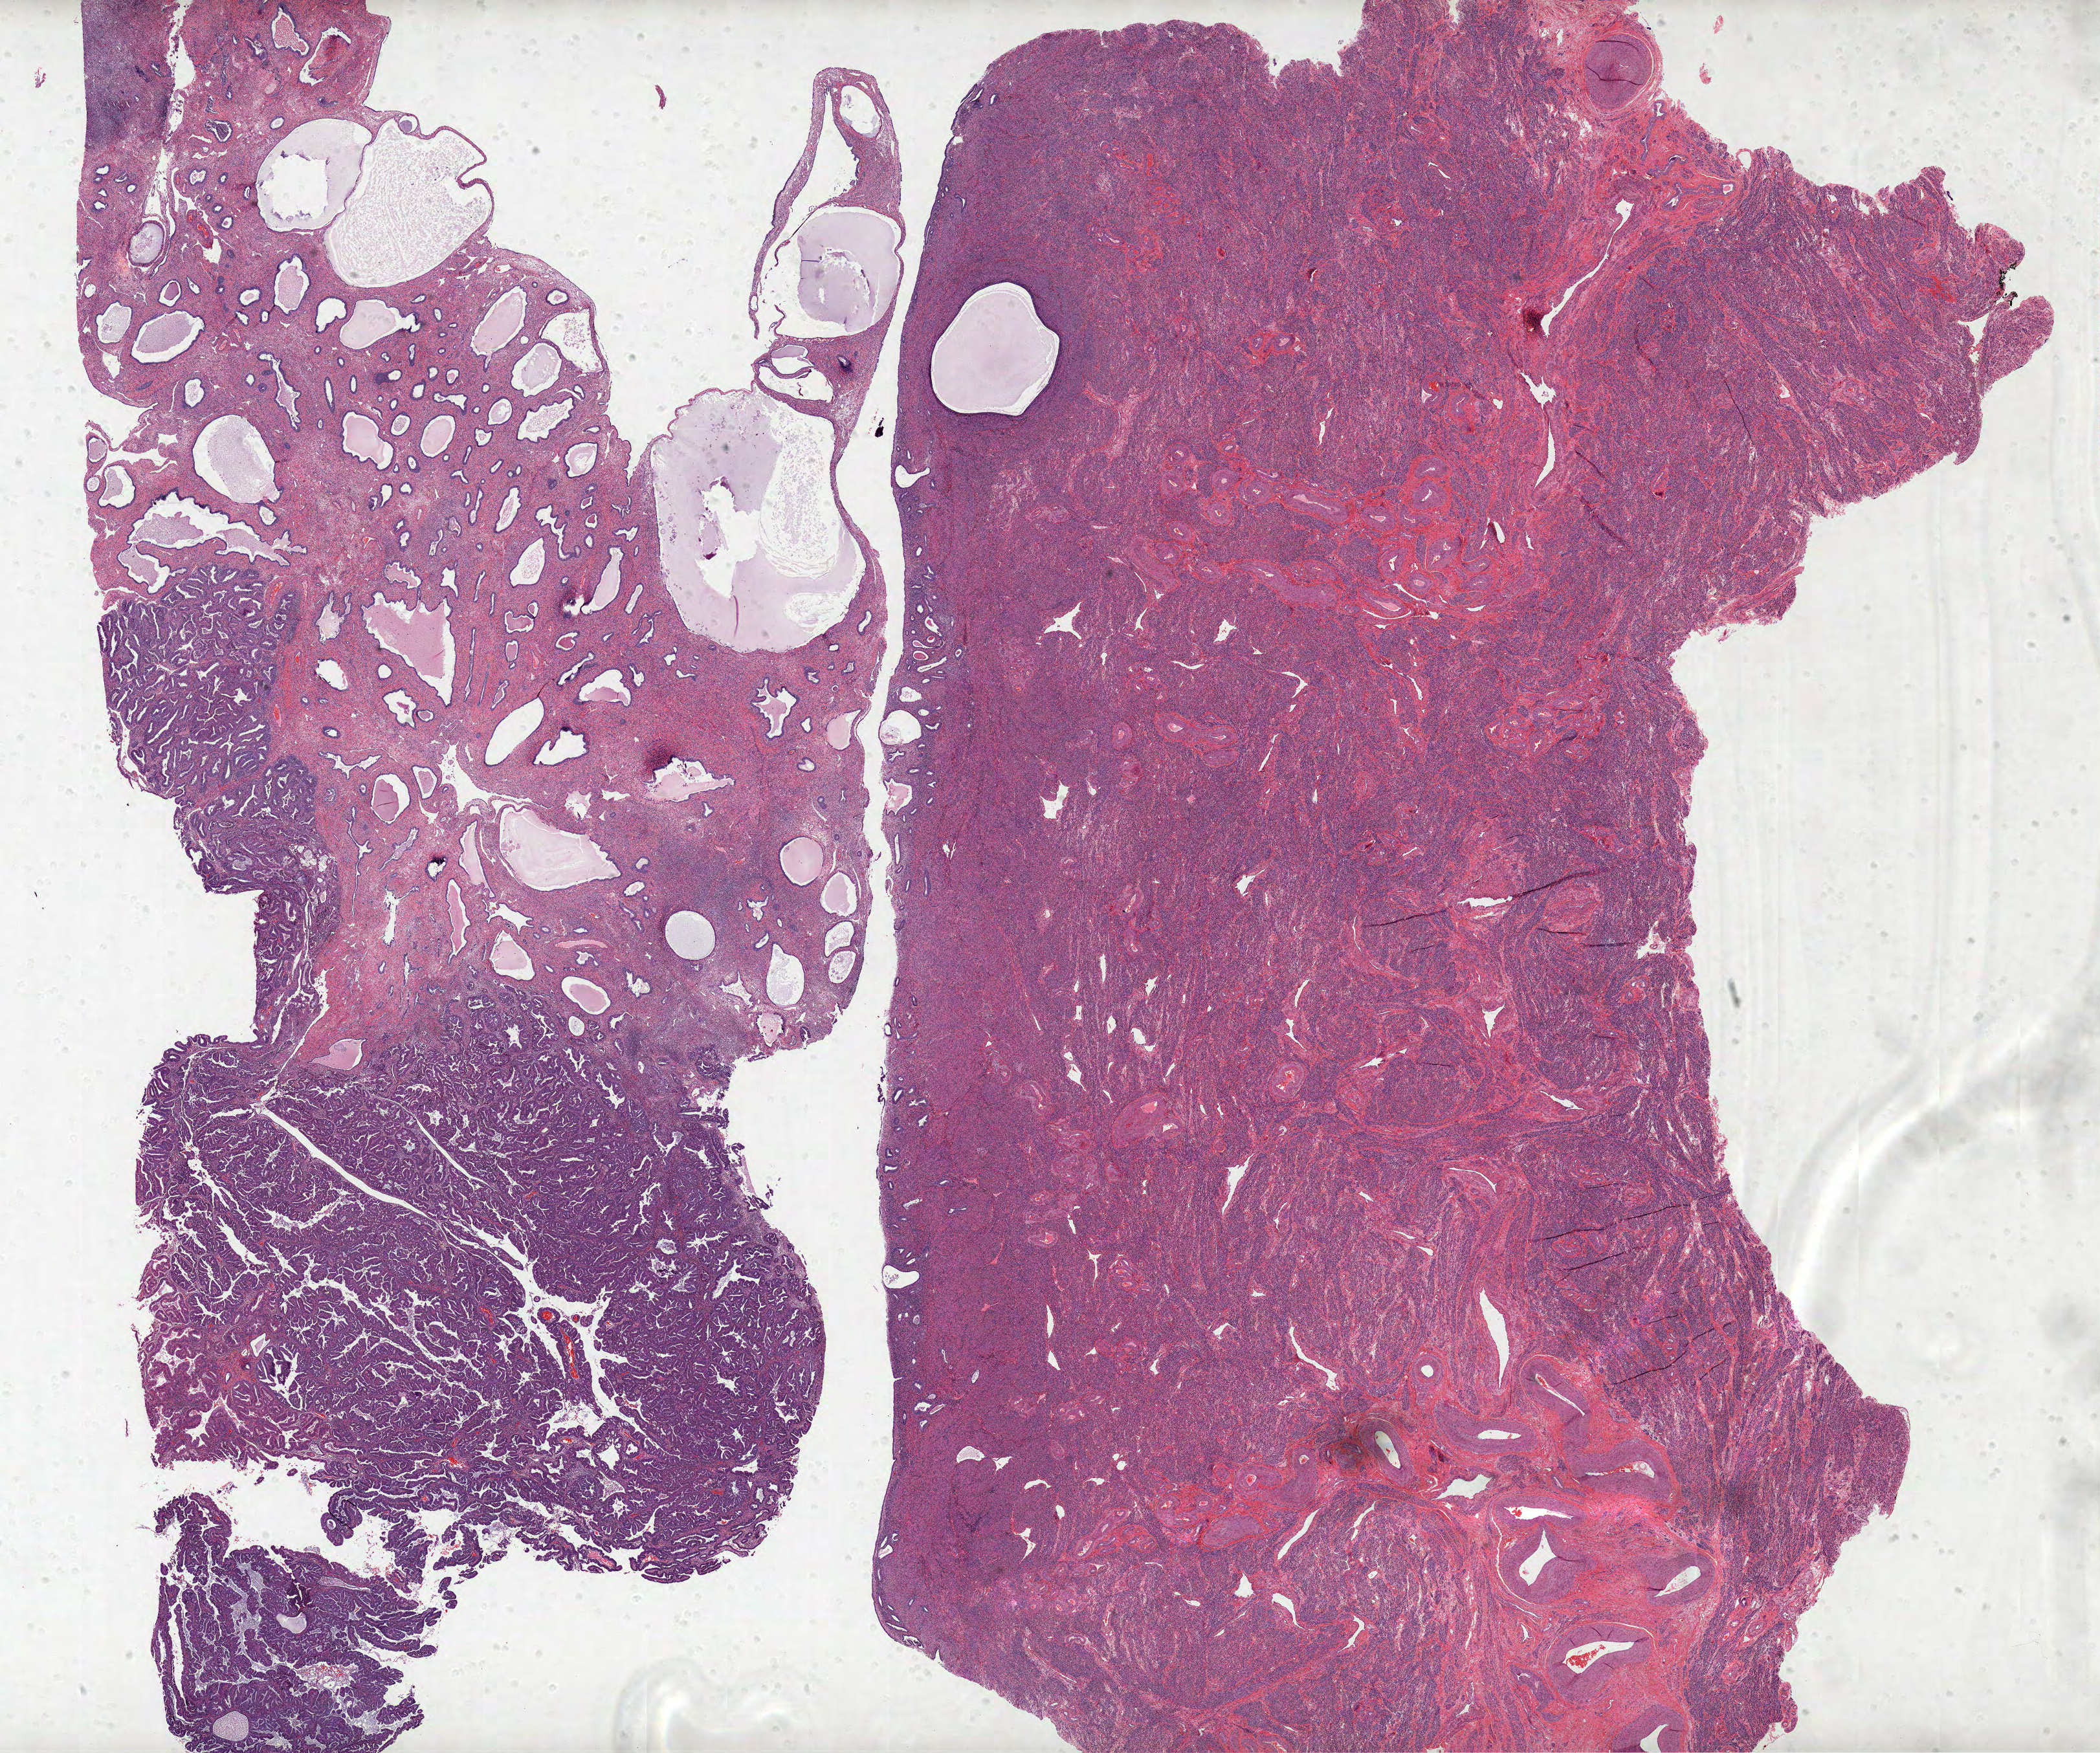
Whole-slide histology image, H&E, whole scanned area (about 25.9 x 21.6 mm) shown as a low-resolution overview; formalin-fixed paraffin-embedded (FFPE) diagnostic section; primary tumour sample from the uterus. Female patient; age at initial diagnosis 60 years. Histologic grade: G3 (poorly differentiated).
• lymph nodes positive (case pathology): 0 of 17 examined
• pathologic diagnosis: Serous cystadenocarcinoma, NOS (endometrium)
• FIGO stage: IA